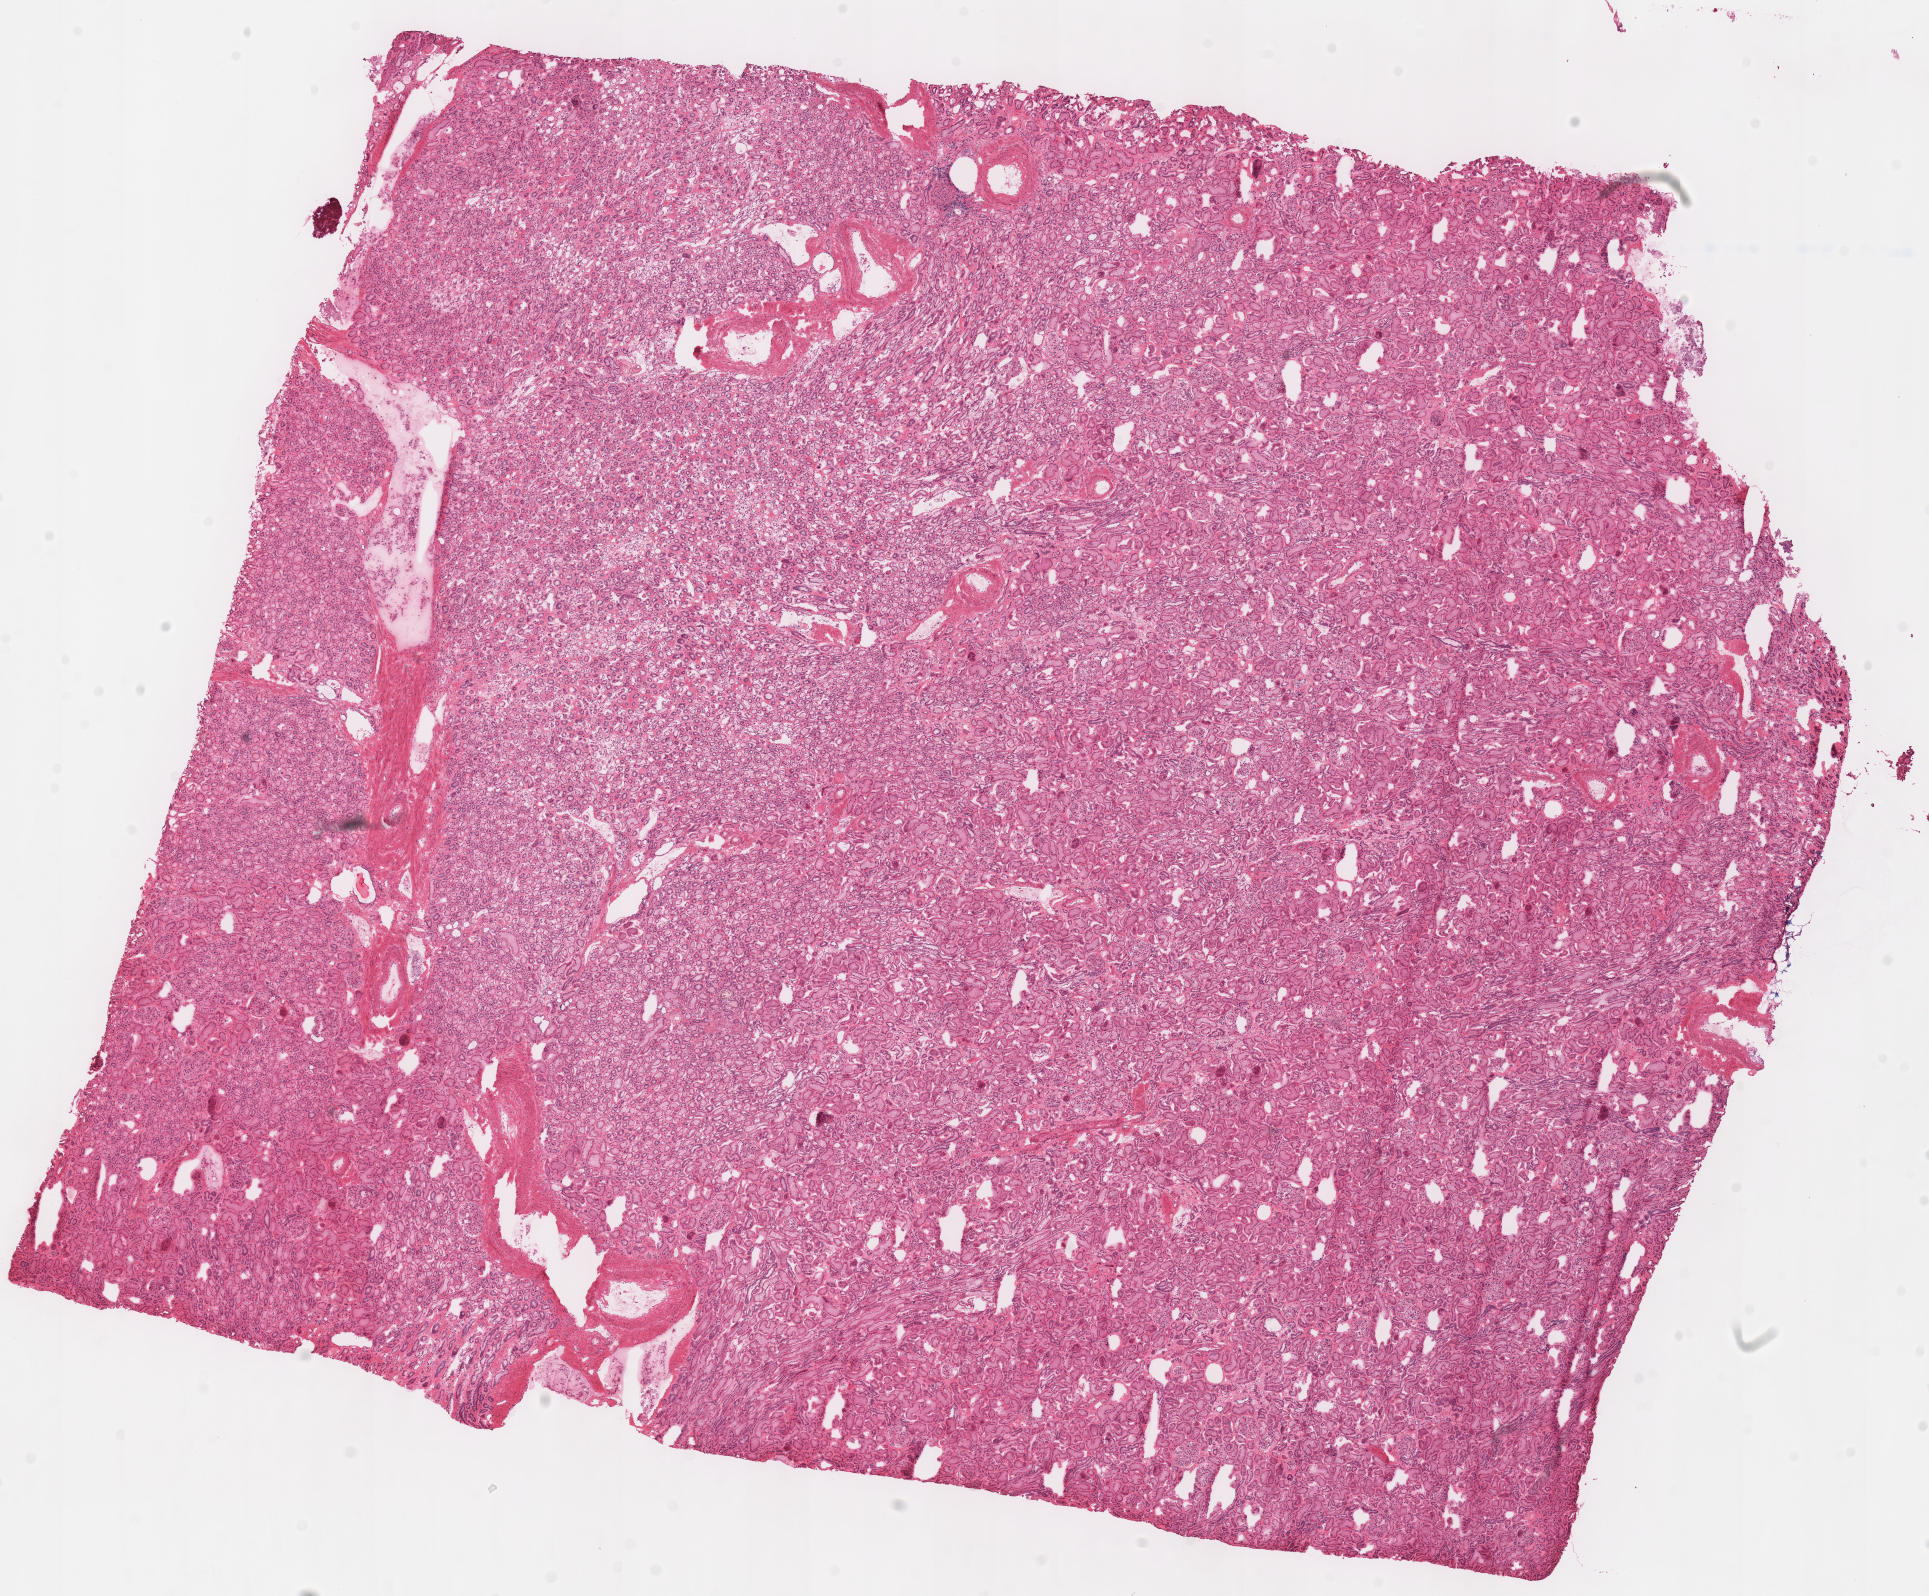
H&E whole-slide image, shown as a low-resolution overview of the whole scanned area (about 15.2 x 12.6 mm); frozen section; kidney, solid tissue normal (non-tumour tissue) sample. Male patient; age at initial diagnosis 62 years.
- this section: solid tissue normal (non-tumour) sample from the same patient
- patient diagnosis: Renal cell carcinoma, chromophobe type